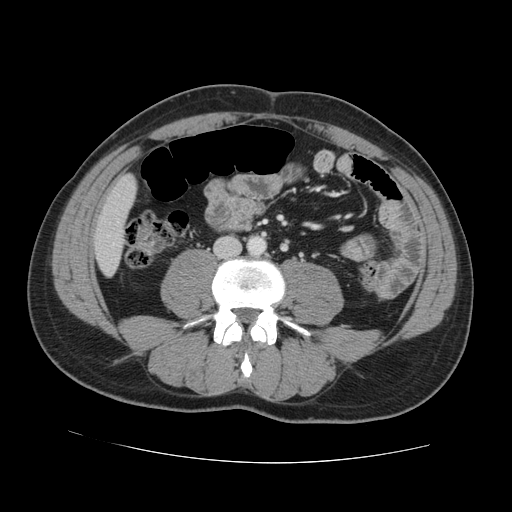
Contrast-enhanced abdominal CT, one axial slice. Intravenous contrast given. Soft-tissue window (W 400 / L 40 HU). 512 × 512 image matrix, field of view 380 × 380 mm. Male patient, age 40 years. From the clinical record (not read from this slice): diagnosis: colorectal cancer liver metastases, imaged before liver resection; multiple liver metastases: yes; largest metastasis: 2.9 cm; disease in both lobes: yes.
Structures marked on this image (outlined manually by an expert reader):
- liver: bounding box <95,177,136,274> (left, top, right, bottom; pixels)